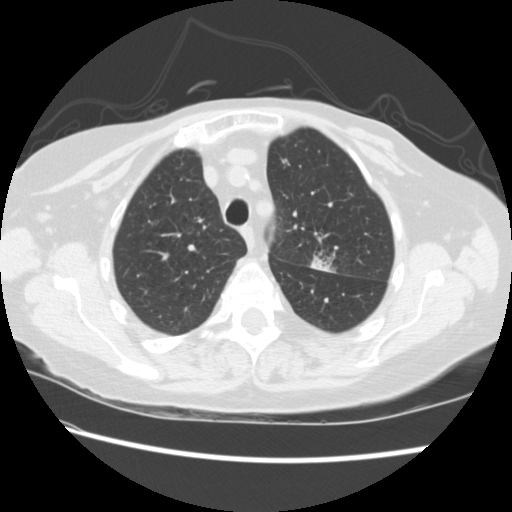
Low-dose screening chest CT, one axial slice; position 168 of 224 along the scan axis; reconstruction kernel STANDARD; lung window (W 1500 / L -600 HU); 2.5 mm slice thickness; 512 × 512 image matrix, field of view 340 × 340 mm.
Outlined on this slice (expert manual segmentation):
- lesion 1 (tumor, upper lobe of left lung): bounding box (x1, y1, x2, y2) in pixels: (311, 256, 333, 272)